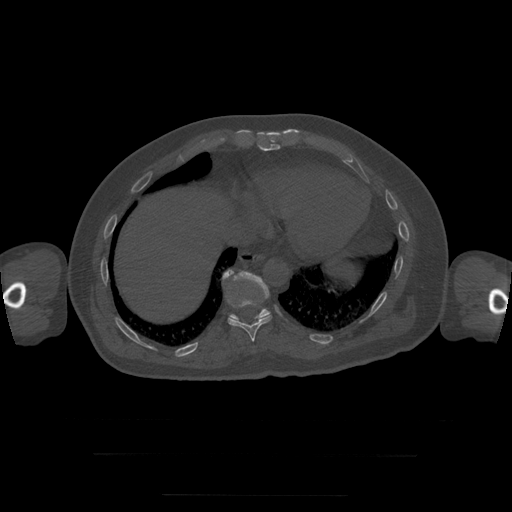
CT including the spine, one axial slice; slice 116 of 397 in the series (ordered by position); reconstruction kernel STANDARD; bone window (W 1800 / L 400 HU); 1.25 mm slice thickness; 512 × 512 image matrix, field of view 510 × 510 mm. Patient age 73 years. Case-level facts recorded for this patient, not image findings: primary cancer: prostate.
Annotated regions visible in this slice (semi-automatic segmentation, software-assisted and operator-edited):
- T10 vertebra: bounding box <223,270,272,342> (left, top, right, bottom; pixels)
- T11 vertebra: <230,271,271,323>